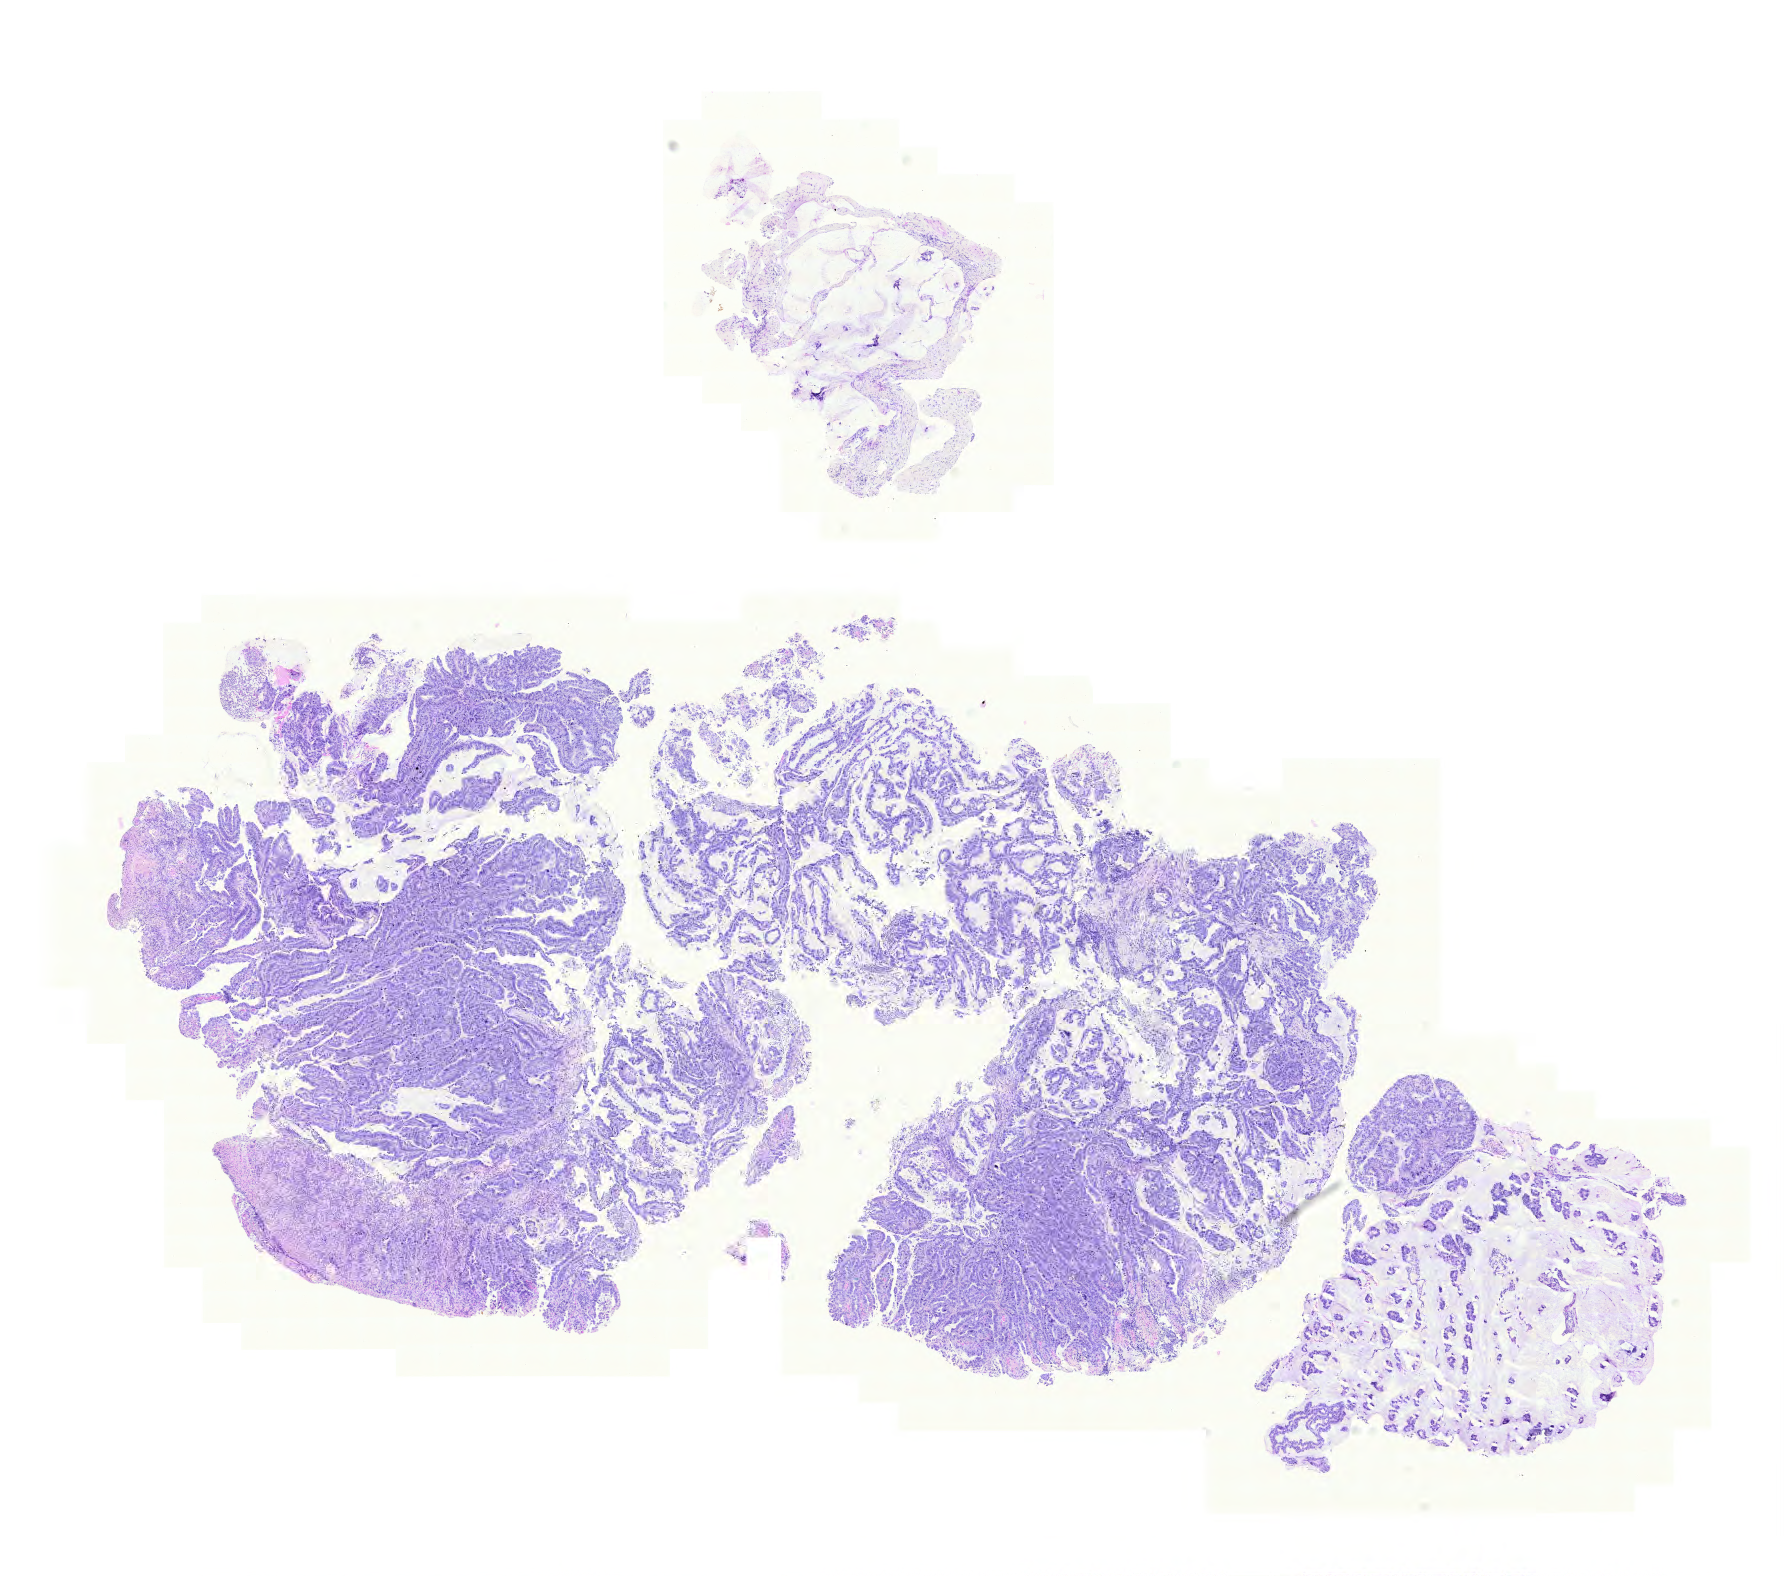
Digitized Hematoxylin and eosin (H&E) stained tissue section (whole slide) — a low-resolution overview of the entire scanned area, about 13.3 x 11.7 mm; FFPE section; primary tumour sample from the stomach. Patient: female, age at initial diagnosis 66 years.
Diagnosis: Adenocarcinoma, intestinal type (body of stomach).